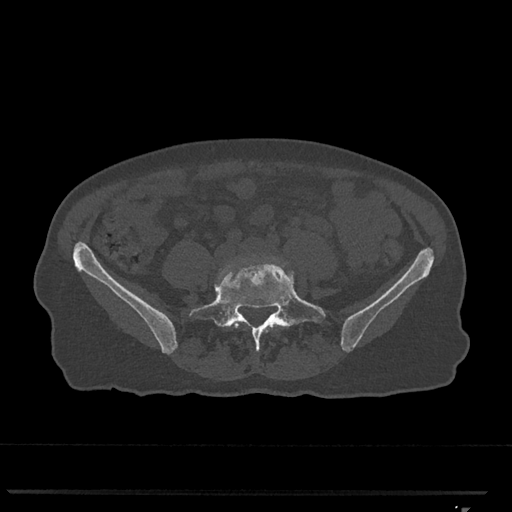
CT including the spine, one axial slice; 120 kVp; bone window (W 1800 / L 400 HU); 0.5 mm slice thickness; 512 × 512 image matrix, field of view 380 × 380 mm. Female patient, age 62 years. Case-level facts recorded for this patient, not image findings: primary cancer: renal.
Structures marked on this image (semi-automatic segmentation, software-assisted and operator-edited):
- L4 vertebra: bounding box [x1, y1, x2, y2] px = [217, 258, 257, 328]
- L5 vertebra: [189, 257, 326, 351]